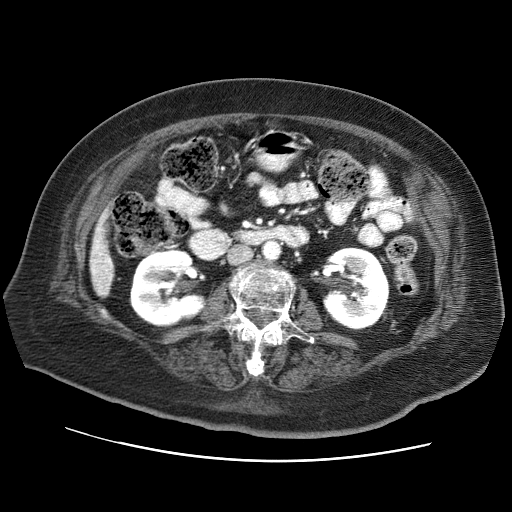
Contrast-enhanced abdominal CT (liver protocol), one axial slice; slice 17 of 73 in the series (ordered by position); 120 kVp; soft-tissue window (W 400 / L 40 HU); 2.5 mm slice thickness; 512 × 512 image matrix, field of view 380 × 380 mm. Case-level facts recorded for this patient, not image findings: diagnosis: hepatocellular carcinoma (patient treated with transarterial chemoembolisation; whether this scan precedes or follows treatment is not stated here); TNM stage (as recorded): Stage-I; Child-Pugh class: A; tumour differentiation: well differentiated.
Outlined on this slice (semi-automatic segmentation, software-assisted and operator-edited):
- liver parenchyma outside the tumour (the mass and vessels are separate outlines, so this box may not span the whole liver): box from (x=90, y=208) to (x=114, y=296) px
- liver vessels: (x=93, y=246)–(x=111, y=273)